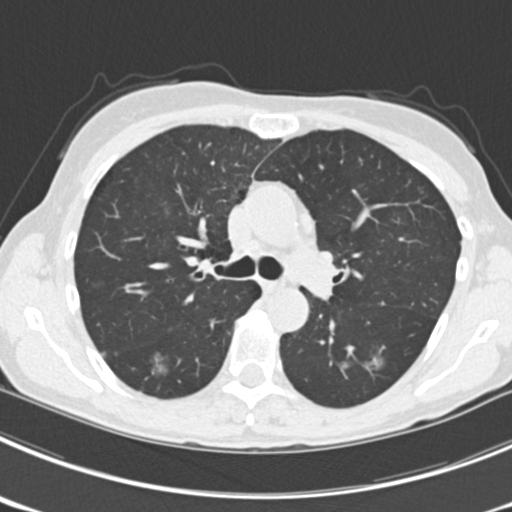
Axial slice from a low-dose chest CT screening exam; third annual screen; lung window (W 1500 / L -600 HU); standard (soft-tissue) reconstruction kernel (B30f); slice 74 of 225 in the series. Female, age 63 years at enrolment.
• 2 expert reader's lesion annotations on this slice (largest first), box from (x=137, y=339) to (x=179, y=383) px; (x=357, y=345)–(x=398, y=382).
• The screening reader recorded 9 non-calcified nodules or masses ≥4 mm on this exam (left upper lobe, right upper lobe, left upper lobe, left lower lobe, right middle lobe, left lower lobe, left lower lobe, right lower lobe, right lower lobe); which of them these boxes mark is not recorded.
• Later outcome: lung cancer diagnosed 15 days after this screen — bronchiolo-alveolar adenocarcinoma, NOS, right upper lobe, right middle lobe, right lower lobe, left upper lobe, left lower lobe, moderately differentiated (G2), stage IV (AJCC 6th edition).